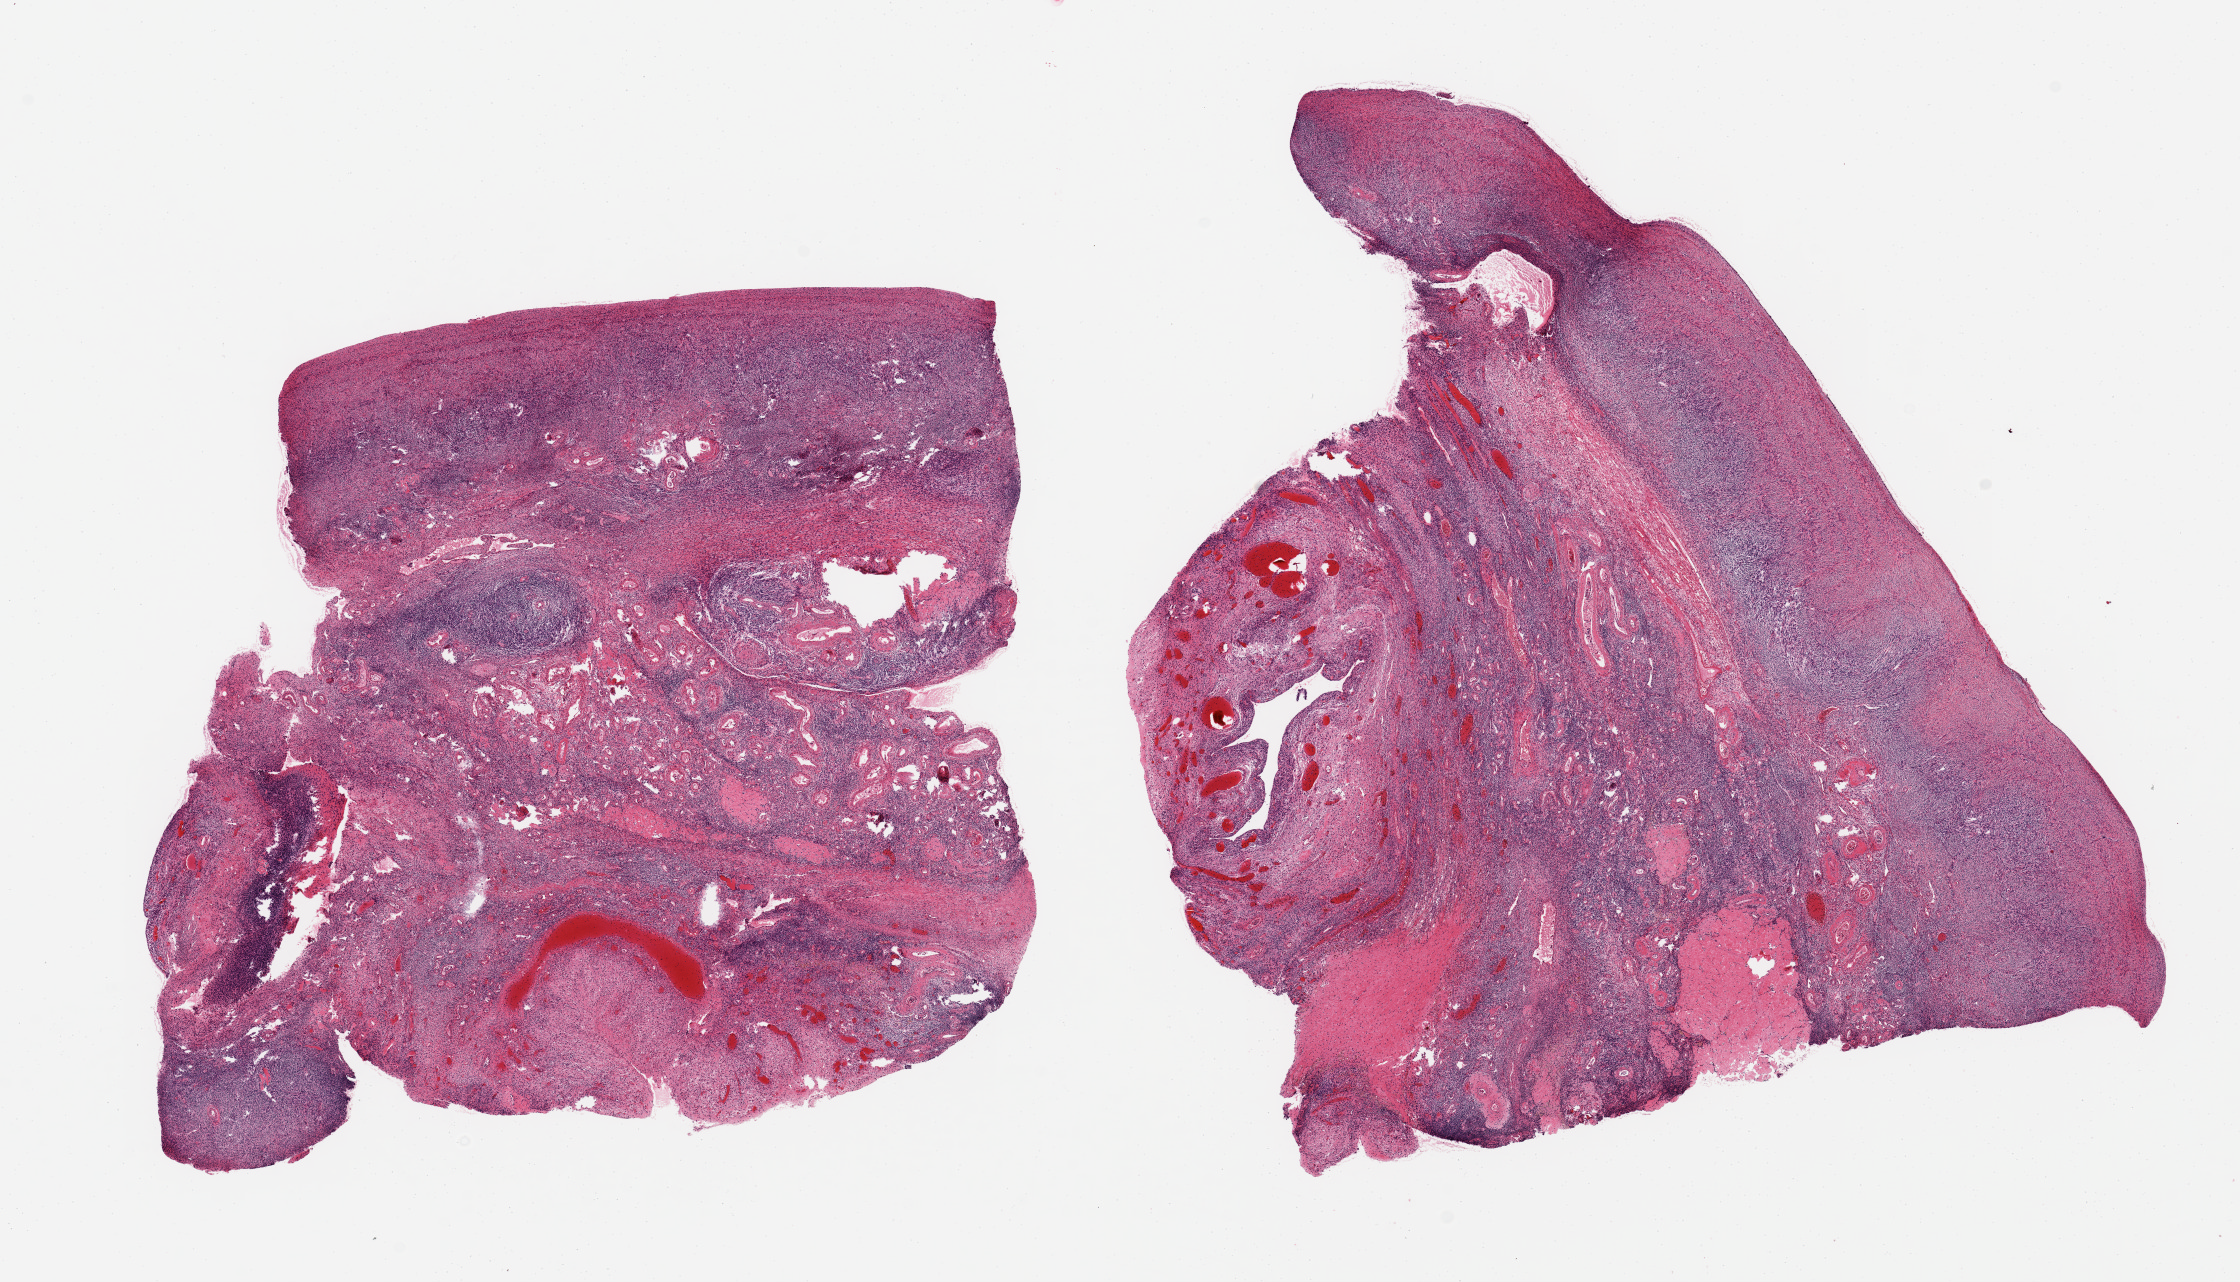
Digitized hematoxylin and eosin (H&E)-stained section, whole scanned area (about 17.7 x 10.1 mm) shown as a low-resolution overview, PAXgene-fixed, paraffin-embedded tissue, sampled site (target tissue): ovary, donor tissue sample. Donor sex: female.
Pathologist's review note for this sample: 2 ~7x6.5mm aliquots, late stage corpus luteum. No ova noted.